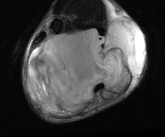
MRI of an extremity soft-tissue mass, one axial slice. Position 23 of 81 along the scan axis. T2-weighted fat-saturated. MR volume resampled by the dataset authors to the PET/CT grid (not the native acquisition matrix). 3.27 mm slice thickness. 165 × 137 image matrix. Male patient. From the clinical record (not read from this slice): histological type: liposarcoma - round cell; grade: high; site of the primary tumour: right calf.
Structures marked on this image (expert contour drawn on MRI and transferred to this co-registered scan by the dataset authors):
- gross tumour volume (mass): bounding box [x1, y1, x2, y2] px = [25, 20, 145, 117]